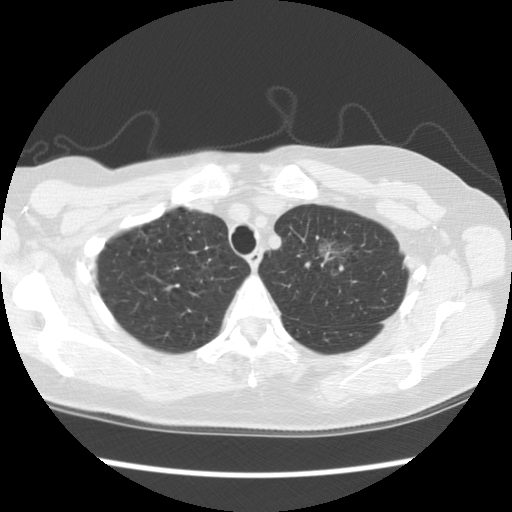
Chest CT (low-dose screening protocol), one axial image. Second screening round (one year after baseline). Lung window (W 1500 / L -600 HU). Standard (soft-tissue) reconstruction kernel (STANDARD). Female participant, aged 65 years at enrolment.
Lesion marked by an expert reader, bounding box [x1, y1, x2, y2] px = [299, 224, 364, 283]. The screening reader recorded 2 non-calcified nodules or masses ≥4 mm on this exam (right upper lobe, left upper lobe); which of them this box marks is not recorded. Official screen result: positive, other. Participant outcome: lung cancer diagnosed 481 days after this screen — adenocarcinoma, NOS, left upper lobe, moderately differentiated (G2), stage IA (AJCC 6th edition), 30 mm at pathology.